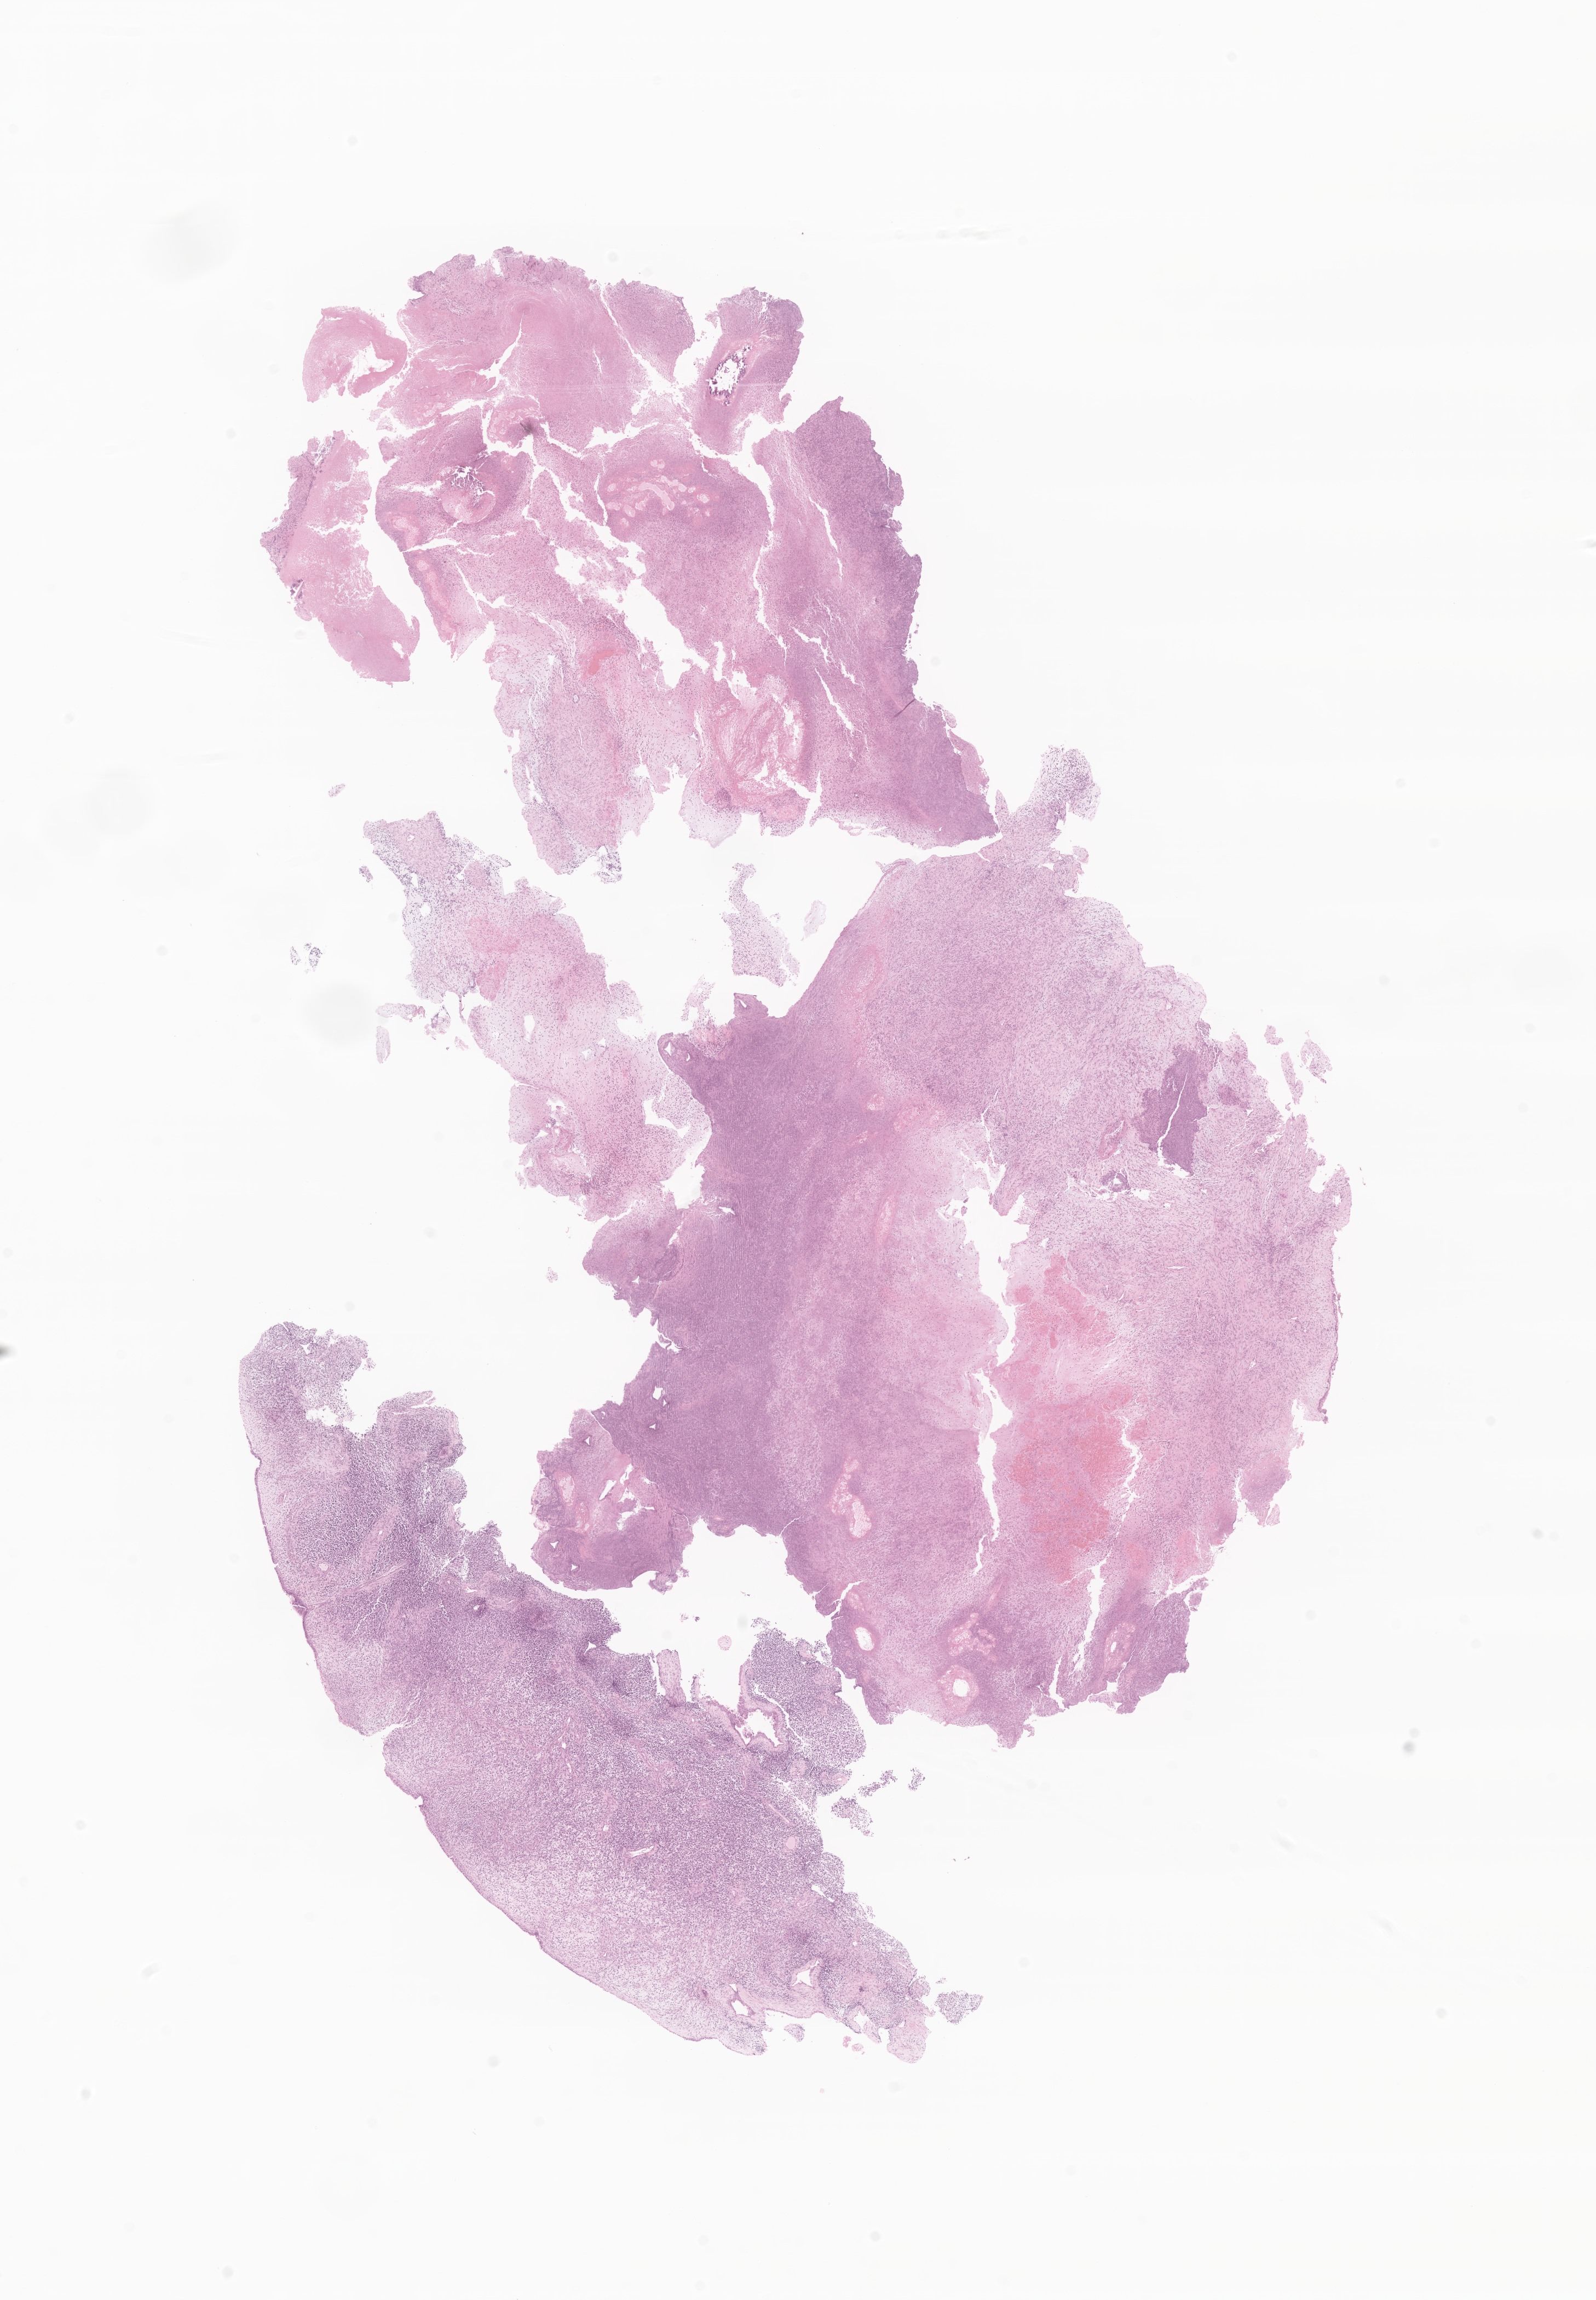
Whole-slide image, hematoxylin and eosin (H&E) stain of tumor tissue from the nasopharynx, a low-resolution overview of the entire scanned area, about 12.3 x 17.7 mm, FFPE section. Patient: female, age 41 months (3 years 5 months).
* diagnosis (ICD-O-3 morphology term): Embryonal rhabdomyosarcoma, NOS